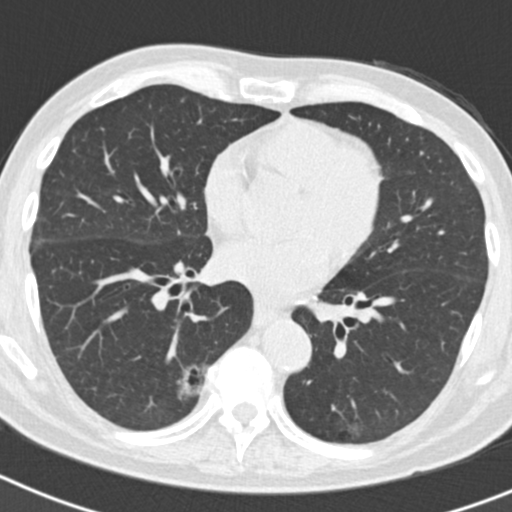
Low-dose screening chest CT, axial slice, second annual screen, lung window (W 1500 / L -600 HU), 2 mm slice thickness, standard (soft-tissue) reconstruction kernel (B30f), slice 95 of 186 in the series, 512 × 512 image matrix. Male participant, aged 70 years at enrolment. Current smoker at enrolment.
- Lesion marked by an expert reader, bounding box [x1, y1, x2, y2] px = [125, 359, 208, 430].
- The screening reader recorded 5 non-calcified nodules or masses ≥4 mm on this exam (right lower lobe, right lower lobe, right upper lobe, right upper lobe, left upper lobe); which of them this box marks is not recorded.
- Official screen result: positive, other.
- Participant outcome: lung cancer diagnosed 622 days after this screen — bronchiolo-alveolar adenocarcinoma, NOS, right lower lobe, poorly differentiated (G3), stage IB (AJCC 6th edition), 30 mm at pathology.